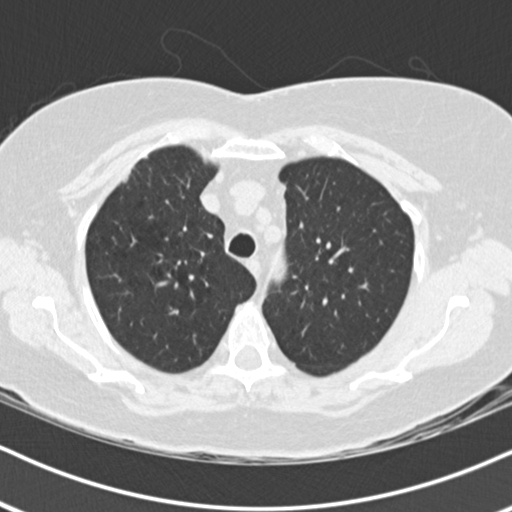
Low-dose screening chest CT, one axial slice; position 142 of 178 along the scan axis; 120 kVp; lung window (W 1500 / L -600 HU); 2 mm slice thickness; 512 × 512 image matrix, field of view 320 × 320 mm.
Annotated regions visible in this slice (expert manual segmentation):
- lesion 1 (tumor, upper lobe of right lung): bounding box [x1, y1, x2, y2] px = [123, 171, 131, 183]